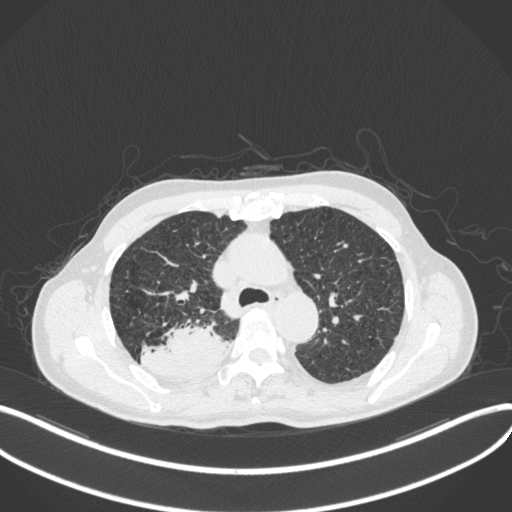
Chest CT, one axial slice. Reconstruction kernel B31f. 120 kVp. Lung window (W 1500 / L -600 HU). 1 mm slice thickness. 512 × 512 image matrix, field of view 400 × 400 mm. Patient: male, 79 years. Case-level facts recorded for this patient, not image findings: clinical TNM (as recorded): T3 N0 M0.
Annotated regions visible in this slice (rectangle marked by the reading radiologist):
- lung tumour (recorded histology: adenocarcinoma): bounding box (x1, y1, x2, y2) in pixels: (138, 319, 232, 385)